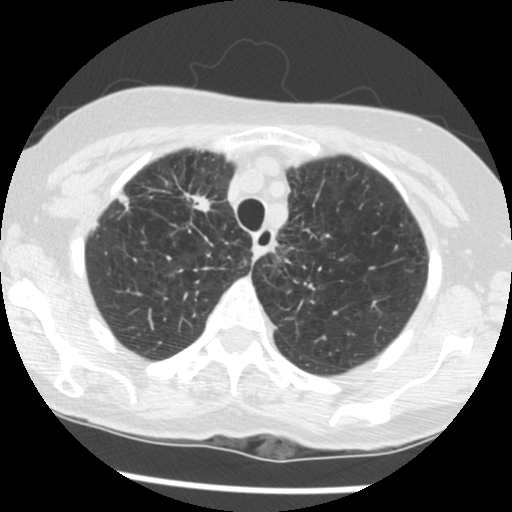
Chest CT (low-dose screening protocol), one axial image, second annual screen, lung window (W 1500 / L -600 HU), standard (soft-tissue) reconstruction kernel (STANDARD), slice 24 of 124 in the series, 512 × 512 image matrix. Female, age 70 years at enrolment. Former smoker at enrolment.
Expert reader's lesion annotation, bounding box [x1, y1, x2, y2] px = [157, 175, 223, 230]. Screening reader's record for this exam (one nodule recorded; not confirmed to be the boxed lesion): non-calcified nodule or mass ≥4 mm, right upper lobe, 11 × 7 mm, spiculated (stellate) margins, soft tissue attenuation, pre-existing on the prior screen: yes; interval growth: yes. Participant outcome: lung cancer diagnosed 248 days after this screen — non-small cell carcinoma, right upper lobe, stage IV (AJCC 6th edition), 30 mm at pathology.